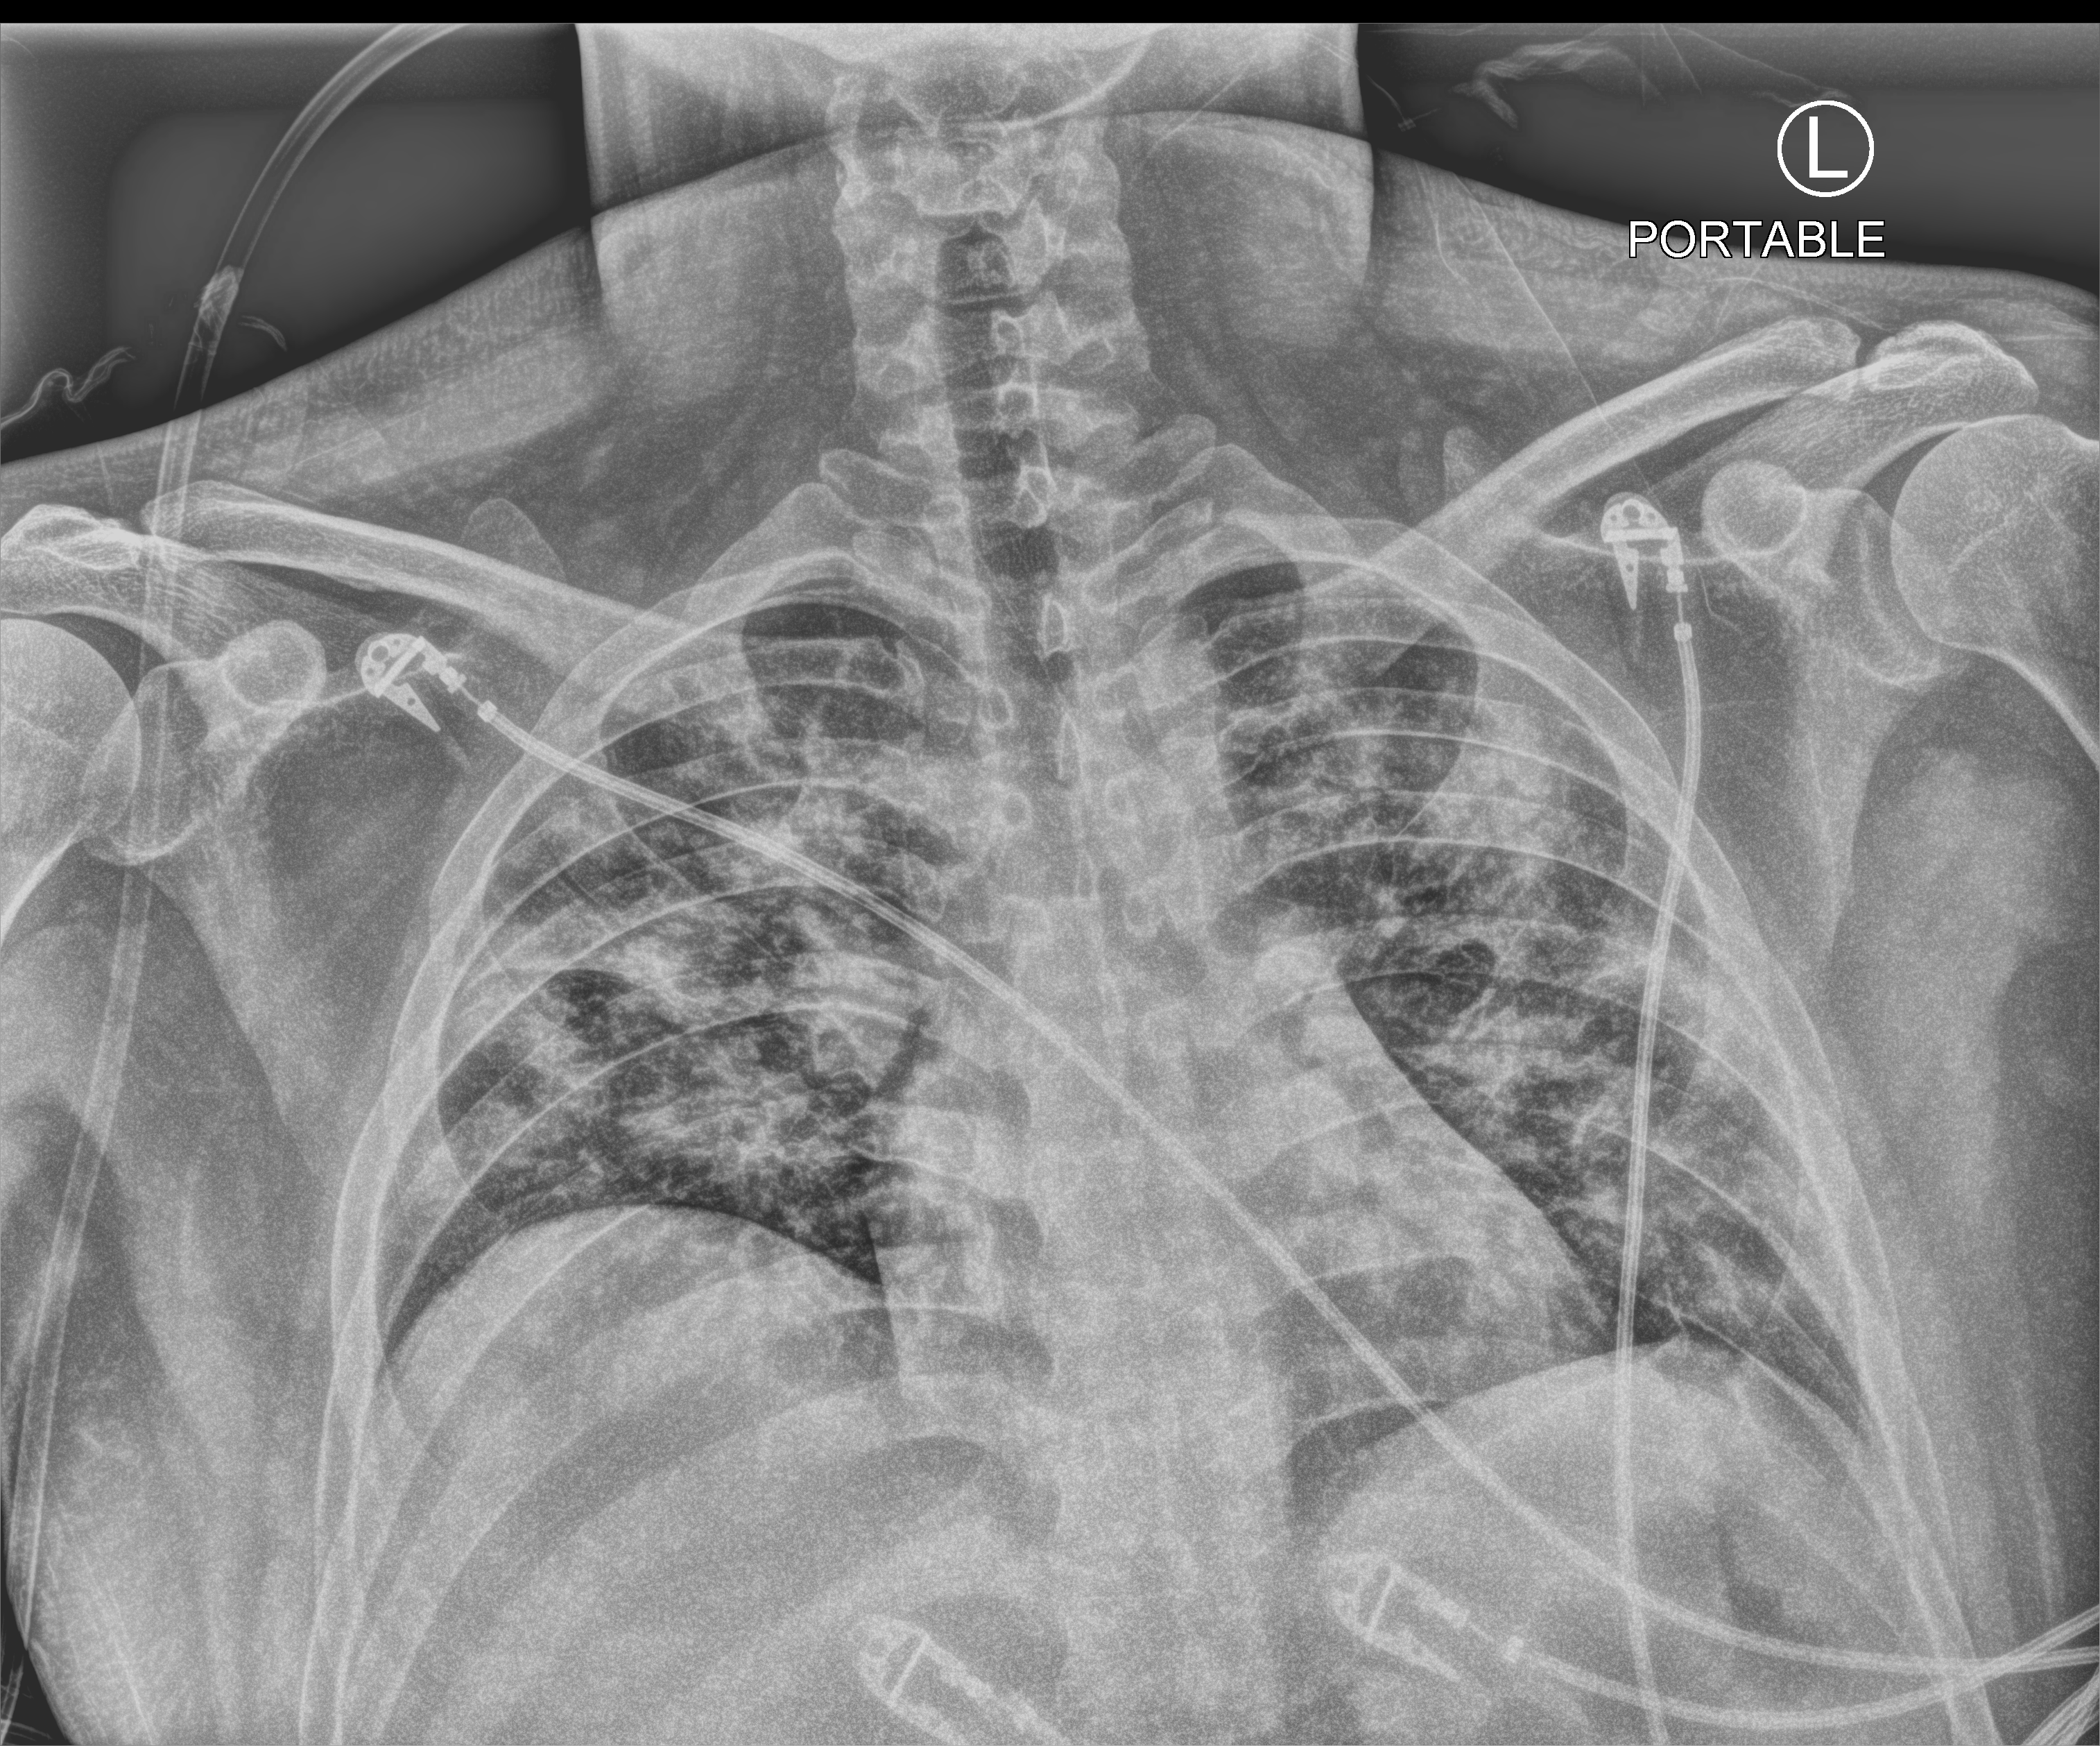
Portable chest radiograph; anteroposterior (AP) projection. Male patient hospitalised with COVID-19, age 18–59 years.
Admission-level facts for this patient (not findings on this image; timing relative to this image not recorded): admitted to intensive care during this hospital stay: yes.